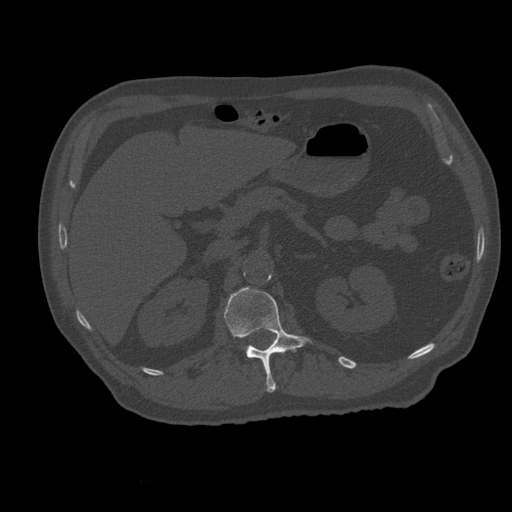
CT including the spine, one axial slice. 120 kVp. Bone window (W 1800 / L 400 HU). 1.25 mm slice thickness. 512 × 512 image matrix. Patient age 73 years. From the clinical record (not read from this slice): primary cancer: prostate; vertebrae with lytic lesions (as recorded): L2.
Structures marked on this image (semi-automatic segmentation, software-assisted and operator-edited):
- L1 vertebra: bounding box [x1, y1, x2, y2] px = [224, 288, 311, 393]